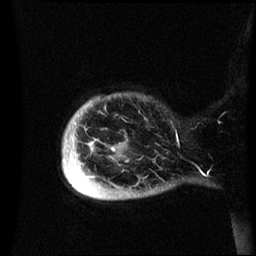
Breast MRI (dynamic contrast-enhanced), one sagittal slice. Slice 4 of 60 in the series (ordered by position). Dynamic contrast-enhanced series, image 2 of 3 at this slice position (ordered by acquisition). 1.5 T. TE 4.2 ms, TR 8.4 ms. 2.4 mm slice thickness. 256 × 256 image matrix, field of view 230 × 230 mm. Female patient, age 49 years.
Structures marked on this image (semi-automatically segmented with operator editing):
- analysis volume of interest (the breast-tissue region the enhancement analysis was run in; not a lesion): bounding box (x1, y1, x2, y2) in pixels: (63, 94, 174, 200)
- tumour enhancement mask (voxels above the 70 % enhancement threshold inside the analysis volume of interest): (64, 147, 115, 162)